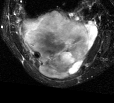
MRI of an extremity soft-tissue mass, one axial slice; slice 23 of 44 in the series (ordered by position); T2-weighted fat-saturated; MR volume resampled by the dataset authors to the PET/CT grid (not the native acquisition matrix); 3.27 mm slice thickness; 114 × 103 image matrix. Female patient. From the clinical record (not read from this slice): histological type: liposarcoma; site of the primary tumour: right thigh.
Structures marked on this image (expert contour drawn on MRI and transferred to this co-registered scan by the dataset authors):
- gross tumour volume (mass): box from (x=20, y=10) to (x=101, y=79) px